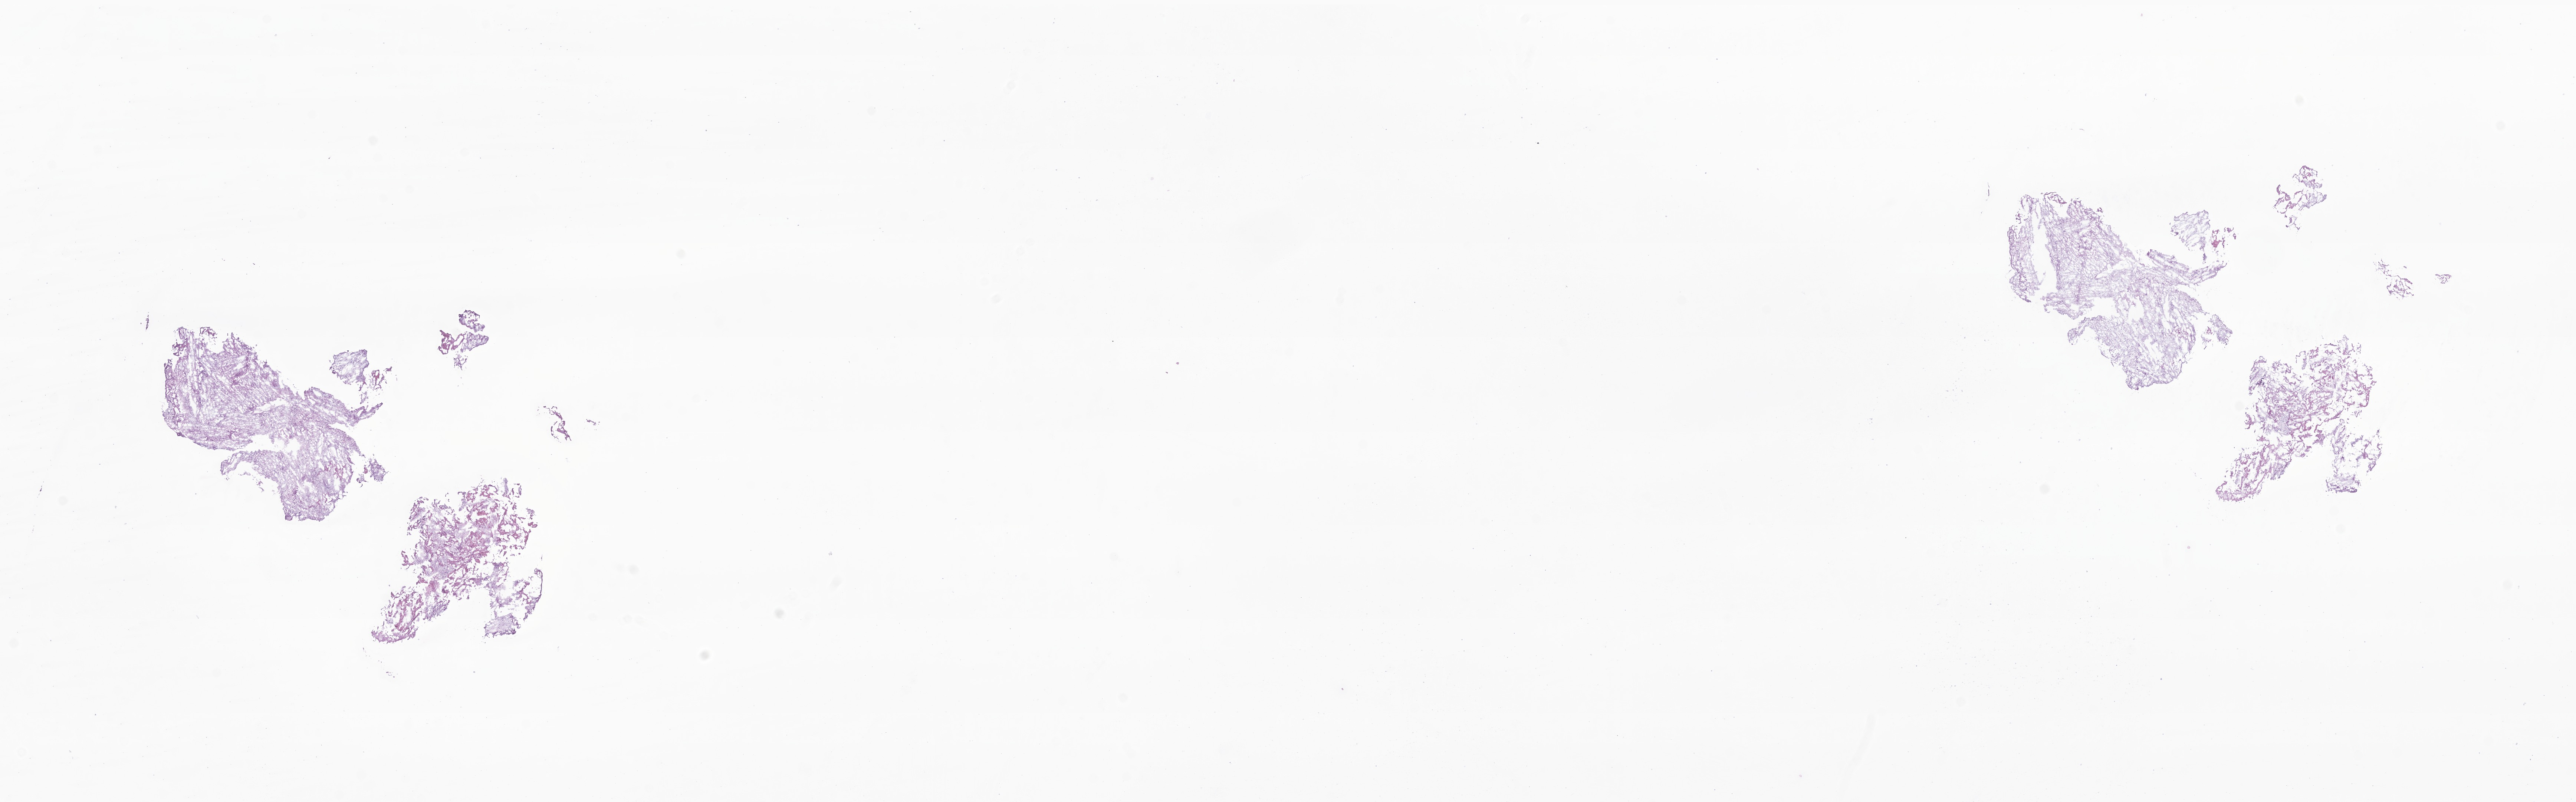
Whole-slide image, H&E stain of tumor tissue from the brain, shown as a low-resolution overview of the whole scanned area (about 29.3 x 9.1 mm); cryosection (OCT / tissue freezing medium). Patient: female, age 46 months.
Diagnosis: Pilocytic astrocytoma.